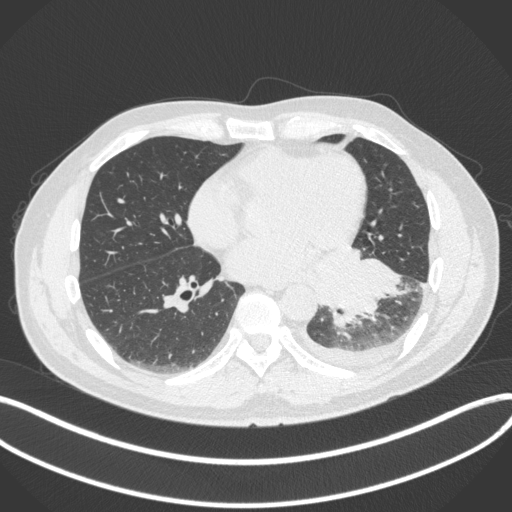
Chest CT, one axial slice; slice 149 of 350 in the series (ordered by position); reconstruction kernel B31f; 120 kVp; lung window (W 1500 / L -600 HU); 1 mm slice thickness; 512 × 512 image matrix, field of view 400 × 400 mm. Patient: male, 58 years. Case-level facts recorded for this patient, not image findings: clinical TNM (as recorded): T3 N1 M1b; histopathological grade: G3.
Annotated regions visible in this slice (rectangle marked by the reading radiologist):
- lung tumour (recorded histology: small cell carcinoma): box from (x=336, y=253) to (x=404, y=342) px